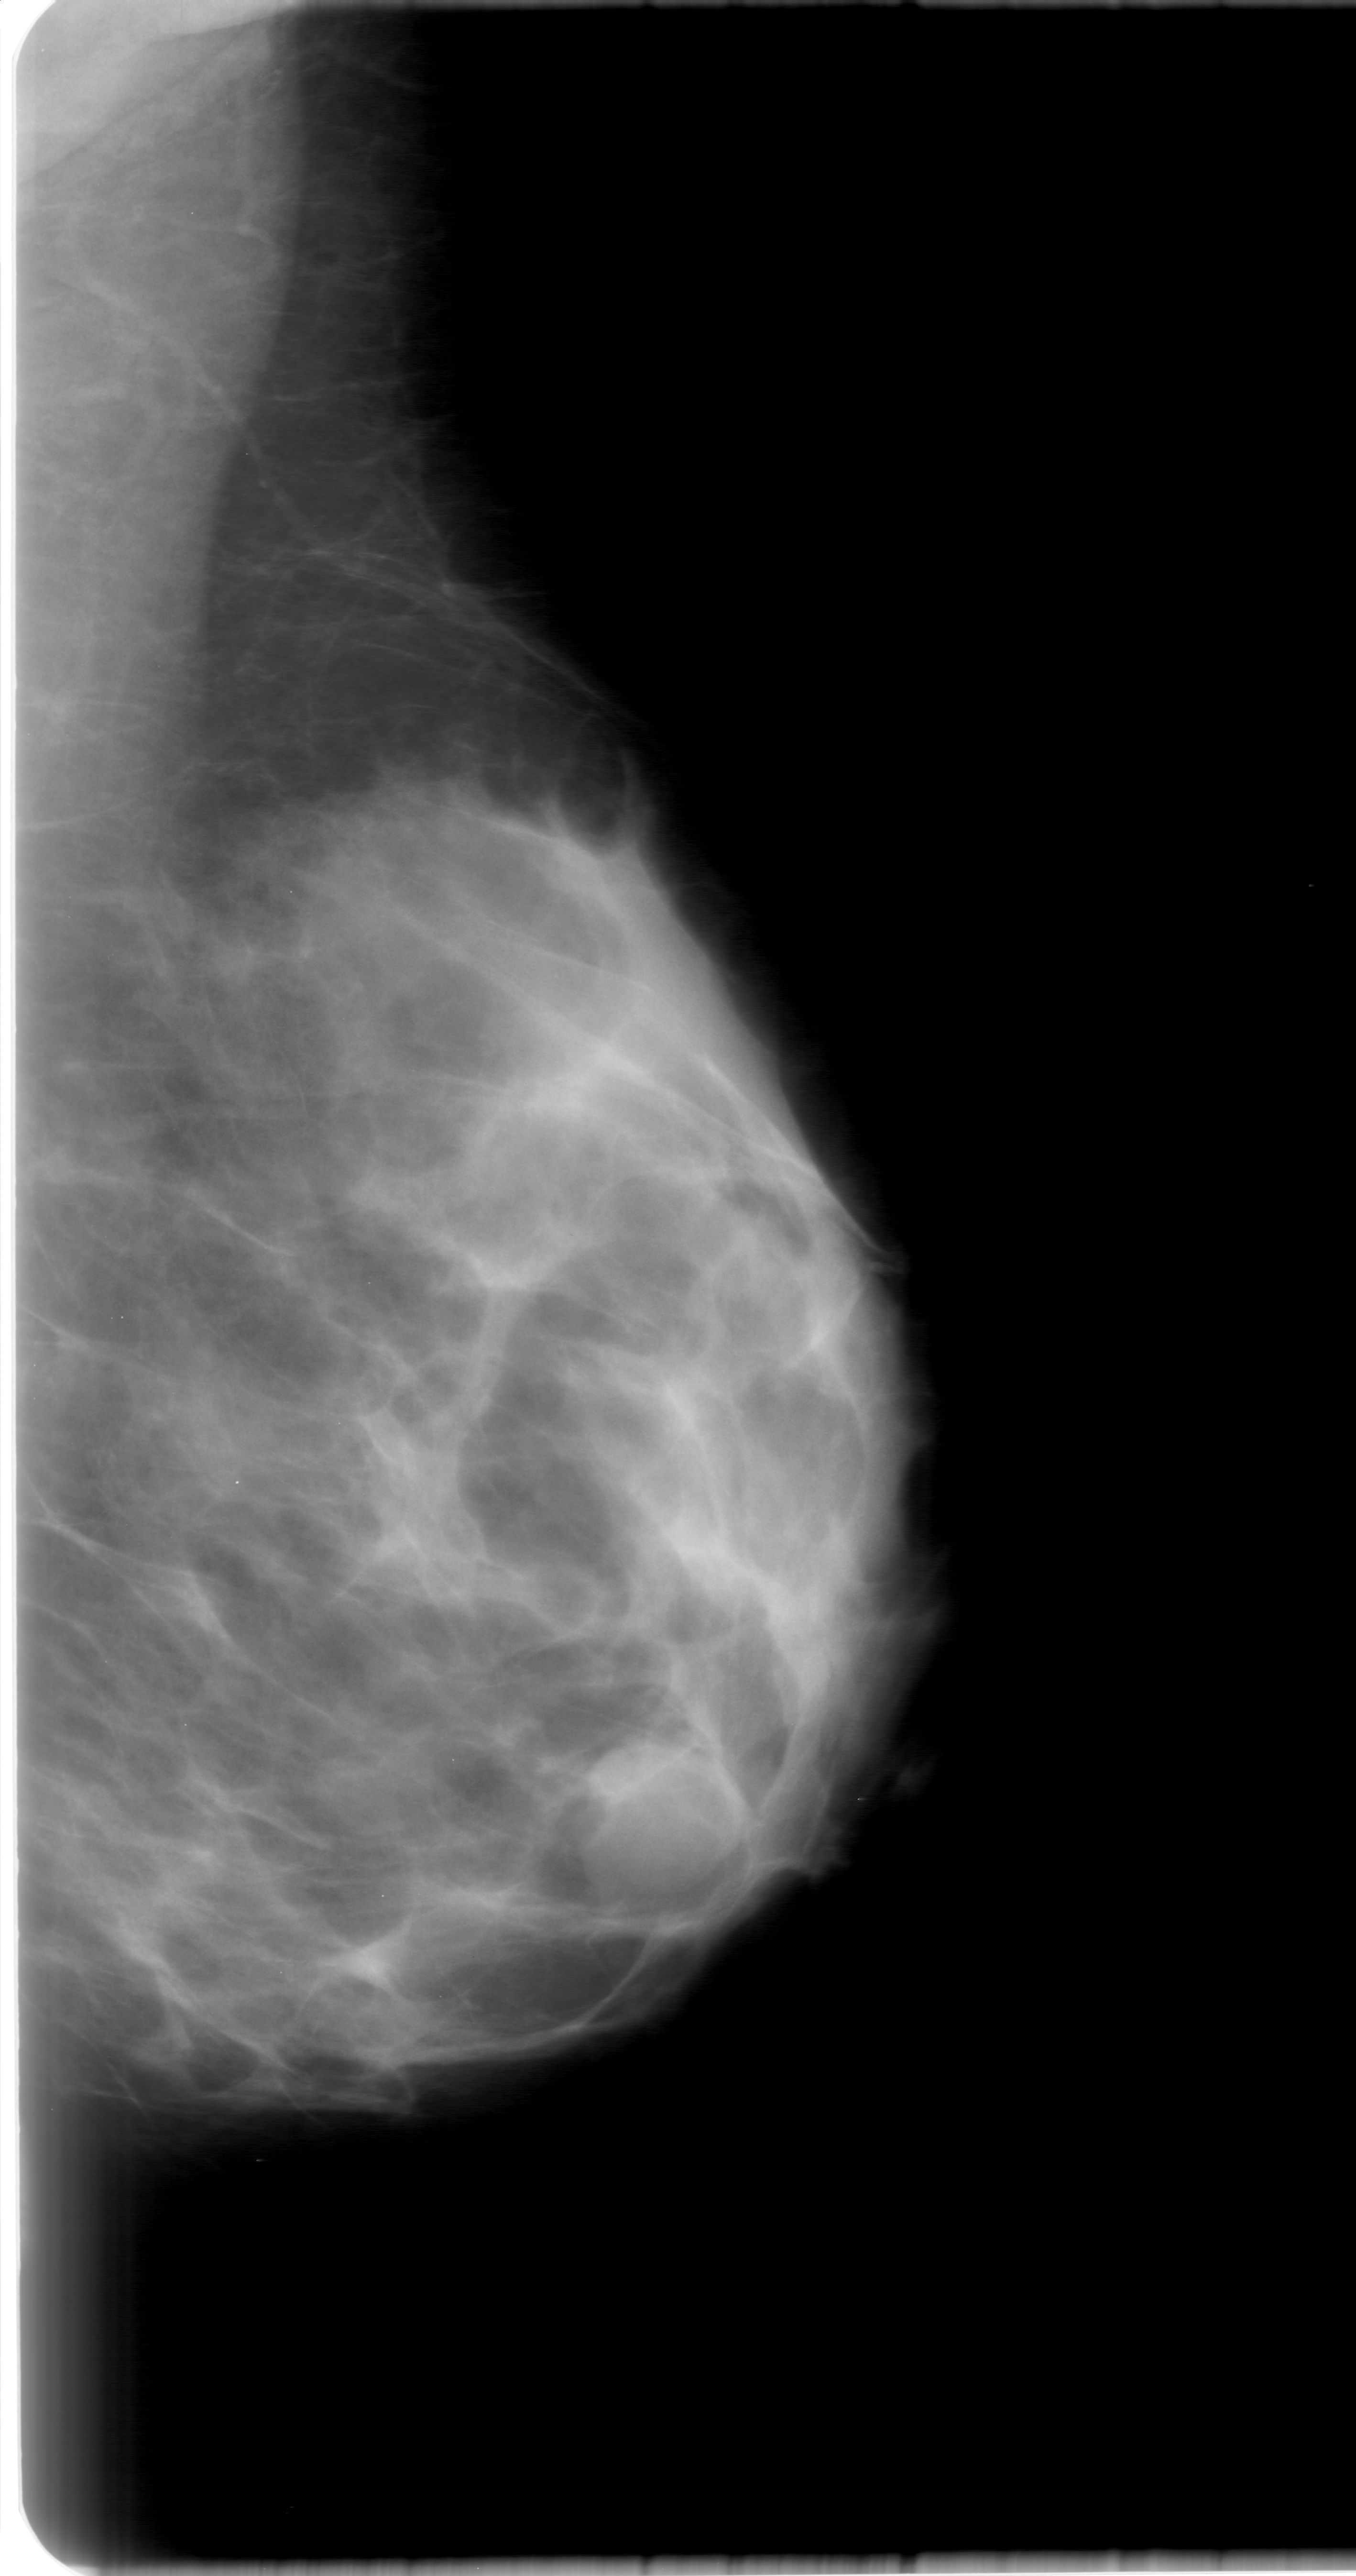
Mammogram (digitized film), left breast, MLO view.
- Abnormality record for this image: mass, shape lobulated, margins circumscribed; BI-RADS assessment category 0 (incomplete: needs additional imaging); subtlety rating 4 on a 1 (subtle) to 5 (obvious) scale; pathology result (as recorded, not read from the image): benign.